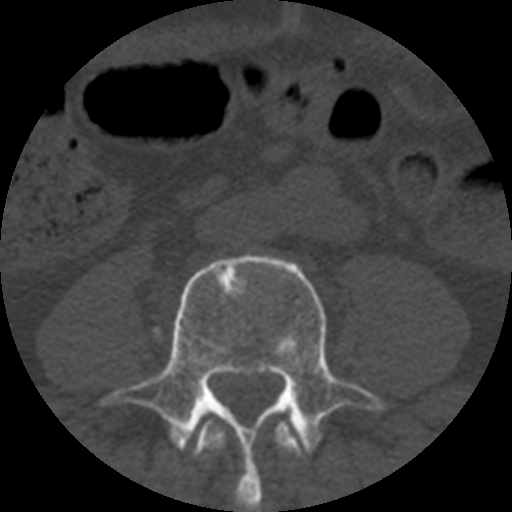
CT including the spine, one axial slice; slice 96 of 508 in the series (ordered by position); reconstruction kernel STANDARD; 120 kVp; bone window (W 1800 / L 400 HU); 512 × 512 image matrix, field of view 160 × 160 mm. Patient age 57 years. Case-level facts recorded for this patient, not image findings: primary cancer: prostate.
Structures marked on this image (semi-automatic segmentation, software-assisted and operator-edited):
- L3 vertebra: bounding box [x1, y1, x2, y2] px = [192, 418, 303, 501]
- L4 vertebra: [101, 254, 385, 512]